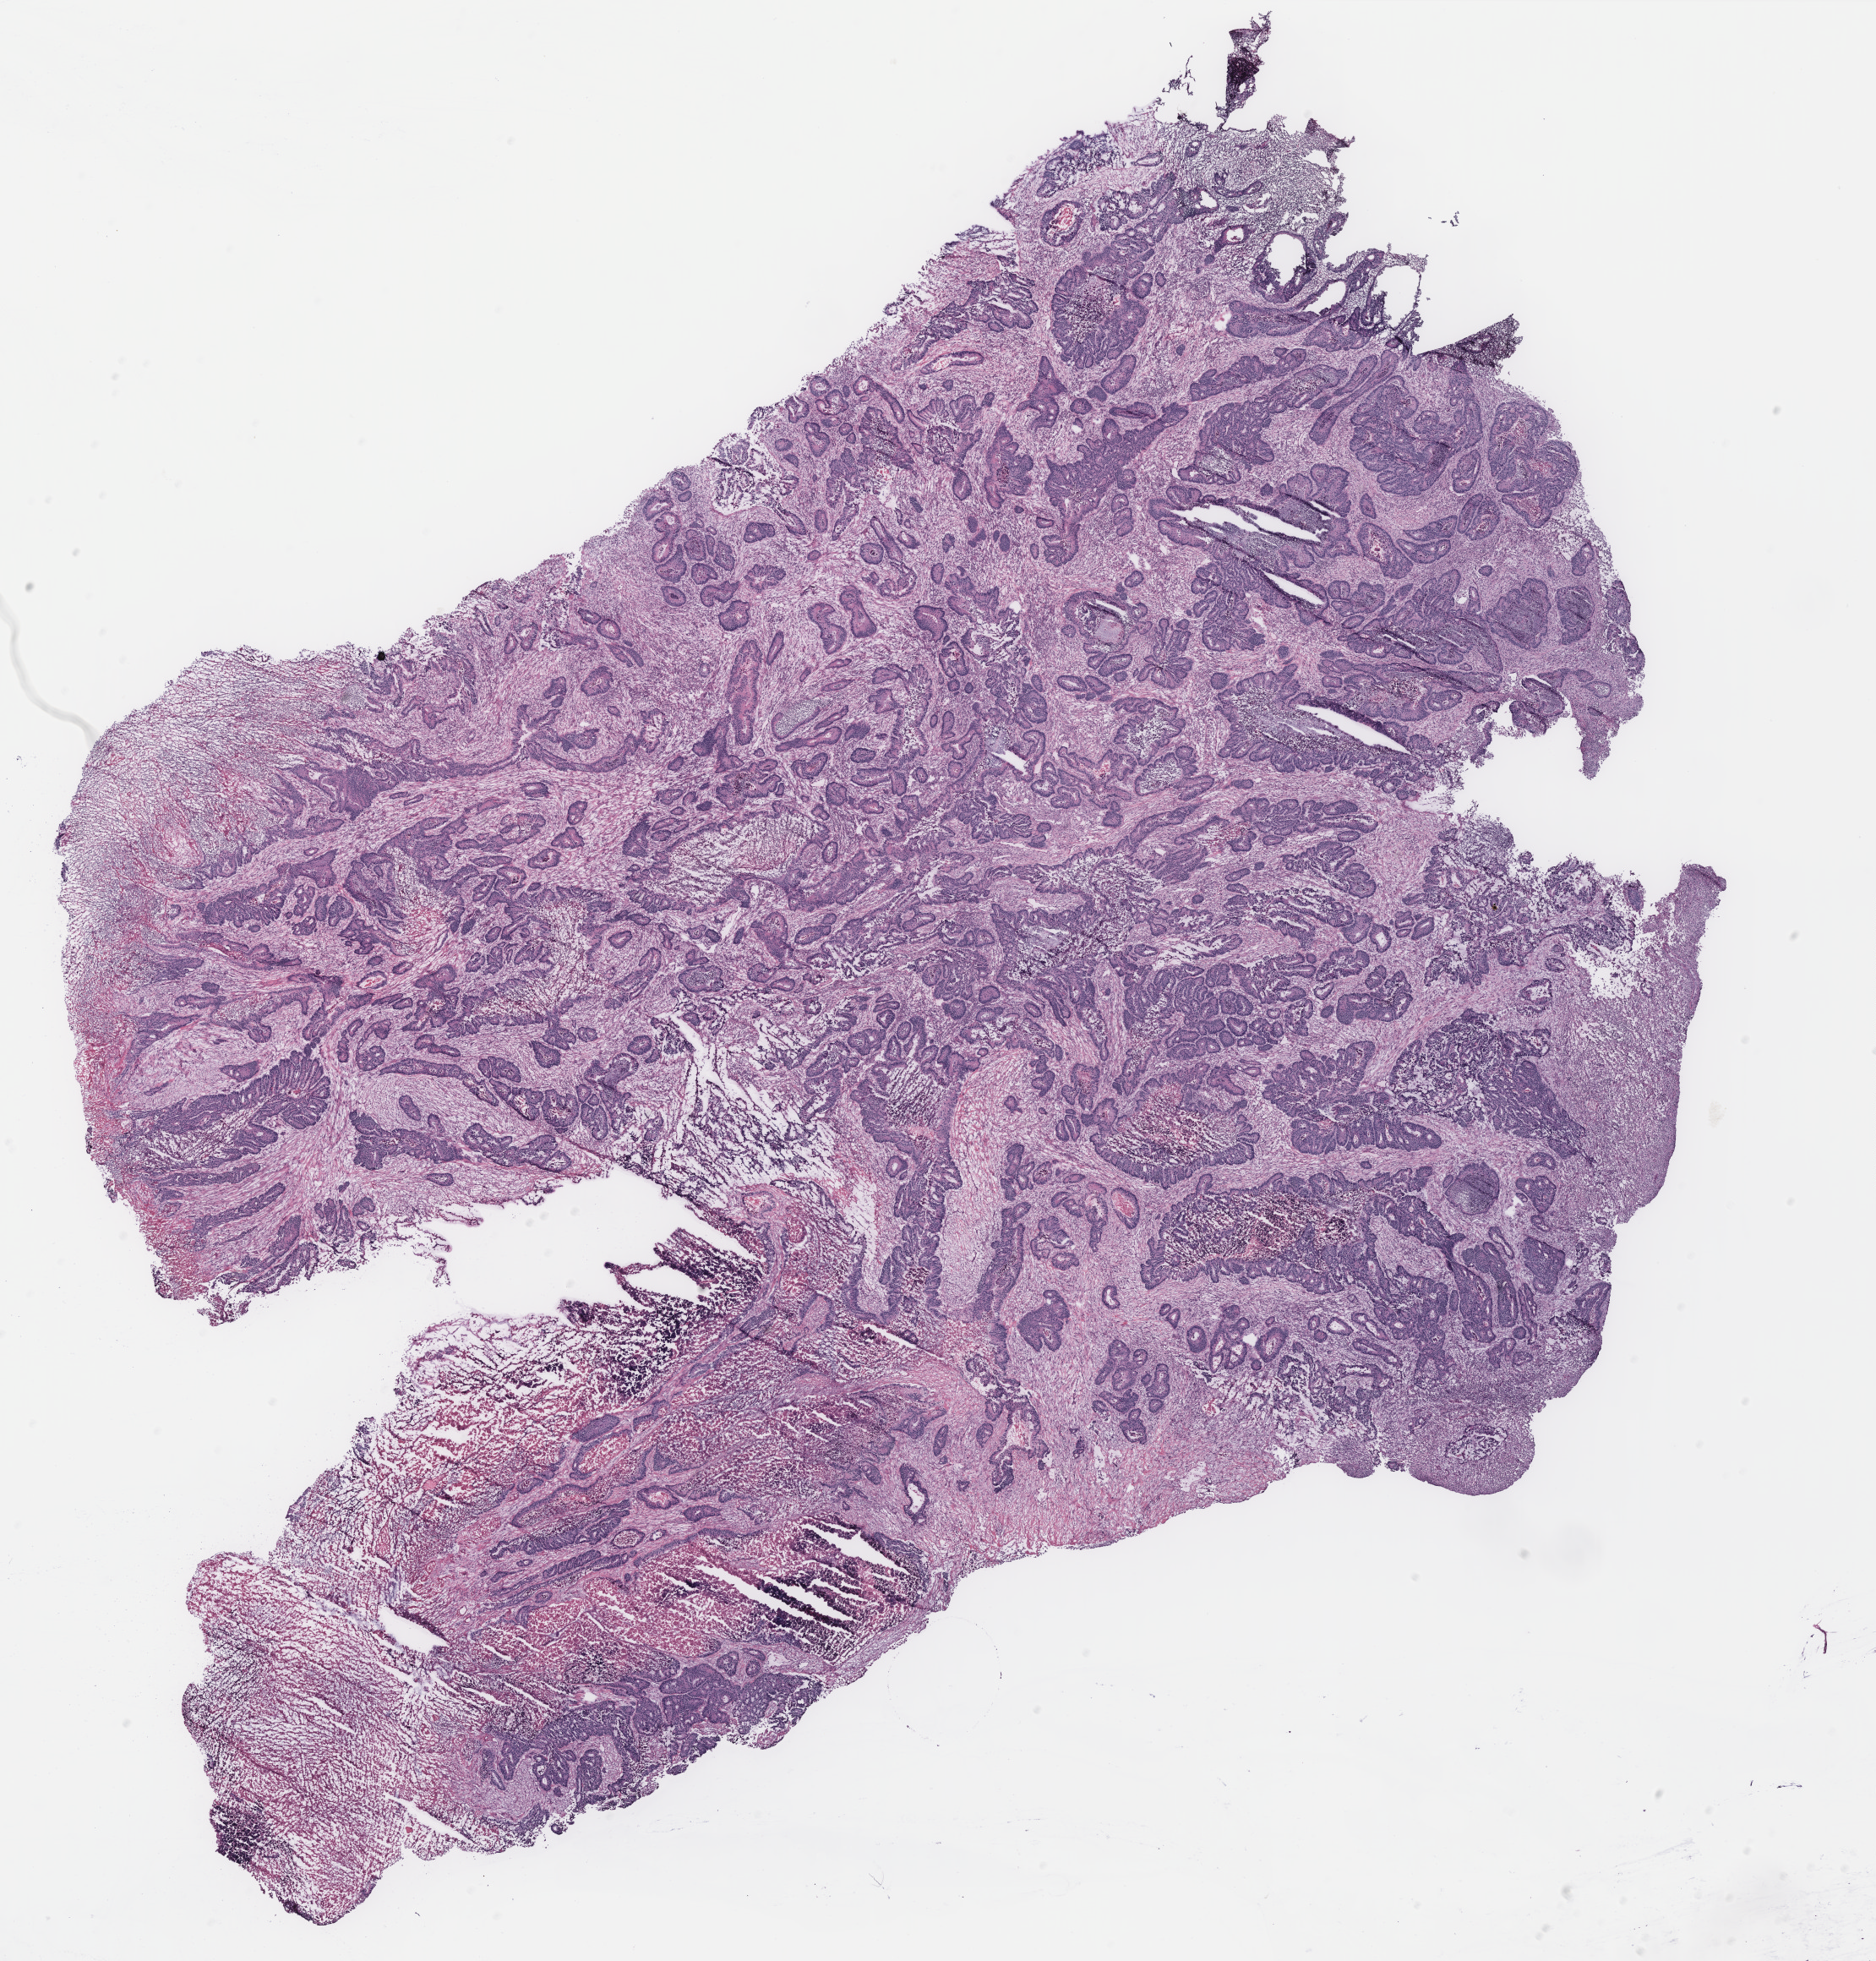
Whole-slide histology image, H&E — whole scanned area (about 17.8 x 18.6 mm, slide scanned at 40x) shown as a low-resolution overview; colon, tissue type not recorded.
Patient diagnosis (cohort enrolment): colon cancer (colon).